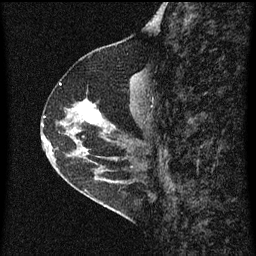
Breast MRI (dynamic contrast-enhanced), one sagittal slice; position 27 of 60 along the scan axis; dynamic contrast-enhanced series, image 2 of 3 at this slice position (ordered by acquisition); 1.5 T; TE 4.2 ms, TR 8 ms; 2 mm slice thickness; 256 × 256 image matrix, field of view 180 × 180 mm. Female patient, age 56 years.
Annotated regions visible in this slice (semi-automatically segmented with operator editing):
- analysis volume of interest (the breast-tissue region the enhancement analysis was run in; not a lesion): bounding box (x1, y1, x2, y2) in pixels: (49, 100, 110, 159)
- tumour enhancement mask (voxels above the 70 % enhancement threshold inside the analysis volume of interest): (76, 100, 101, 123)